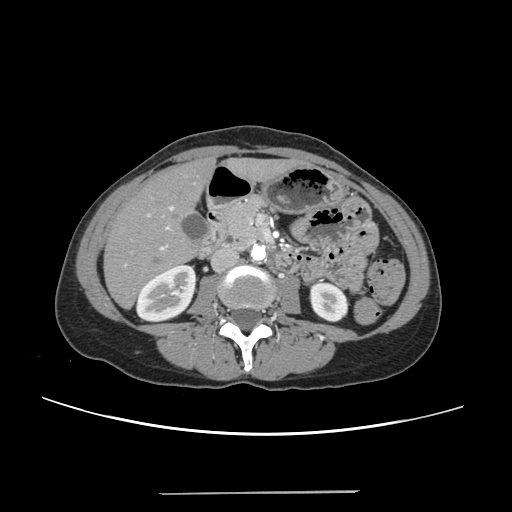
Contrast-enhanced abdominal CT, one axial slice; intravenous contrast given; soft-tissue window (W 400 / L 40 HU); 512 × 512 image matrix, field of view 371 × 371 mm. Female patient, age 60 years. Case-level facts recorded for this patient, not image findings: diagnosis: colorectal cancer liver metastases, imaged before liver resection.
Outlined on this slice (expert manual segmentation):
- liver: bounding box [x1, y1, x2, y2] px = [105, 161, 289, 306]
- planned liver remnant (the part of the liver to remain after resection): [105, 162, 289, 306]
- portal vein (with intrahepatic branches): [123, 206, 173, 267]